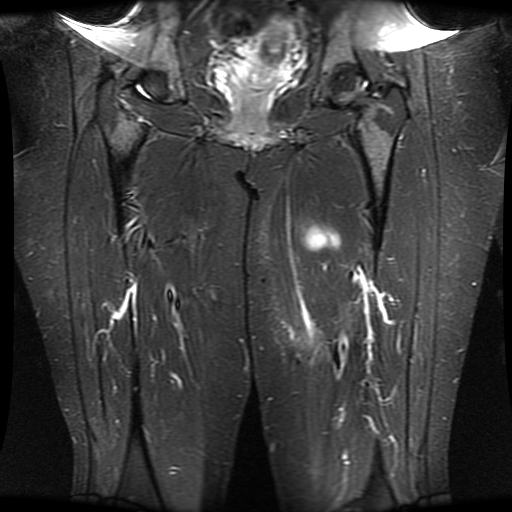
MRI of an extremity soft-tissue mass, one coronal slice. Slice 16 of 30 in the series (ordered by position). STIR. 5 mm slice thickness. 512 × 512 image matrix, field of view 460 × 460 mm. Female patient. Case-level facts recorded for this patient, not image findings: histological type: myxofibrosarcoma; grade: intermediate; site of the primary tumour: left thigh.
Annotated regions visible in this slice (outlined manually by an expert reader):
- gross tumour volume including surrounding oedema: bounding box (x1, y1, x2, y2) in pixels: (302, 225, 341, 251)
- gross tumour volume (mass): (305, 230, 341, 251)